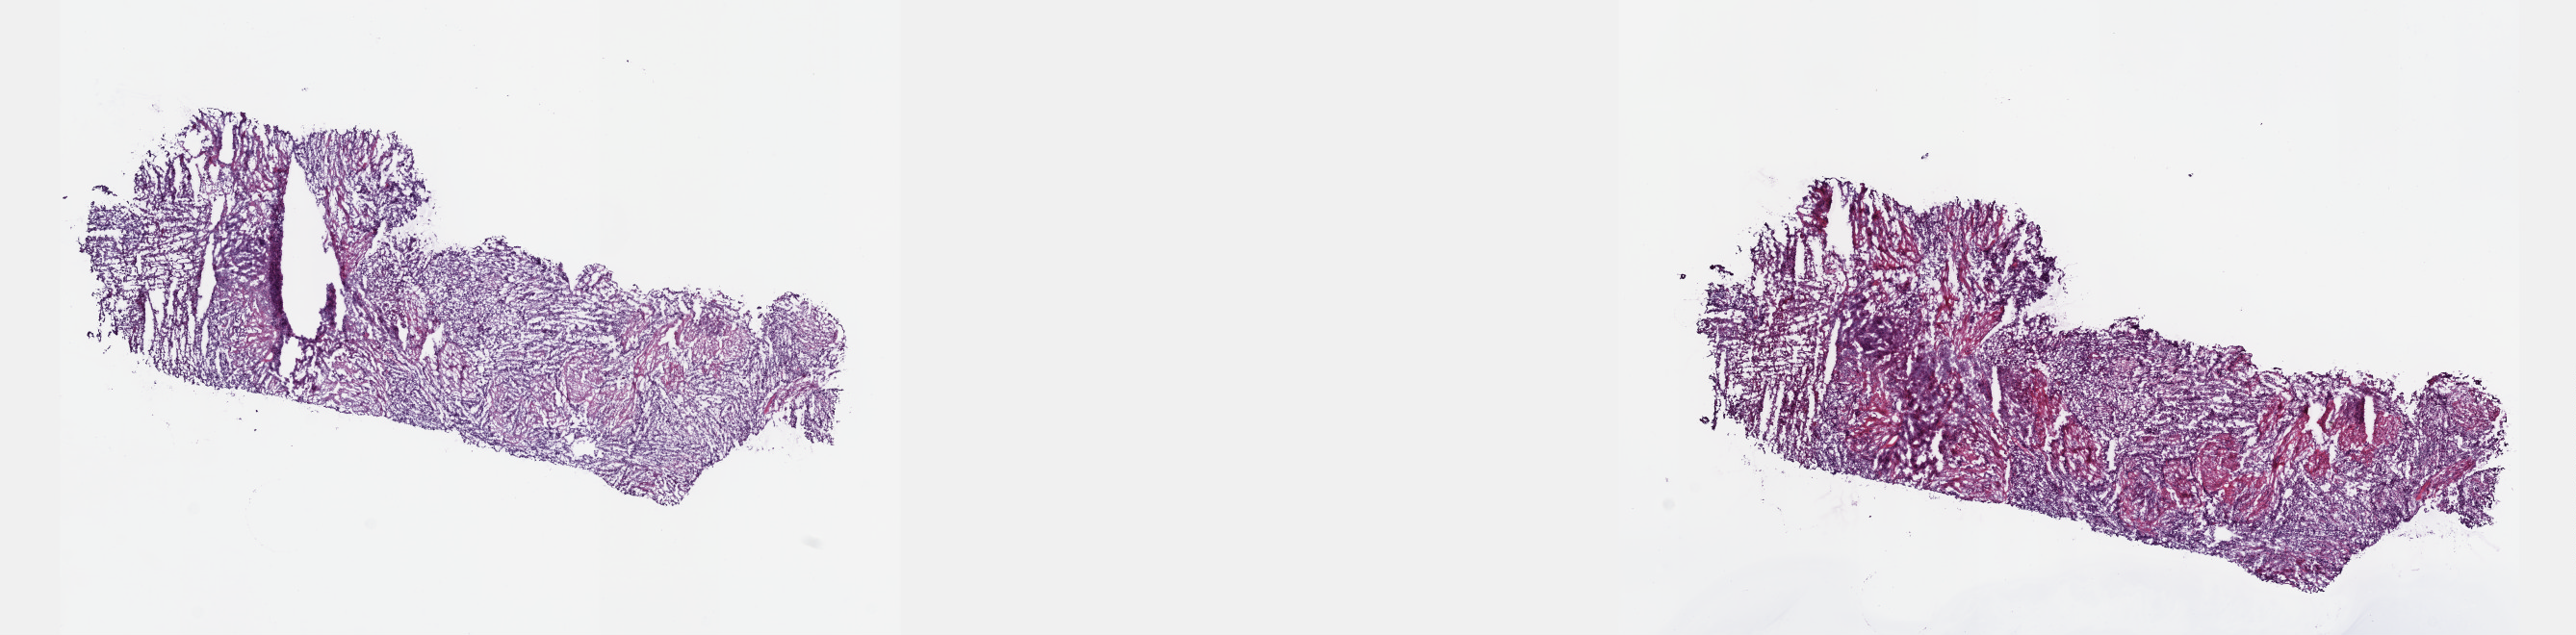
Digitized Hematoxylin and eosin (H&E) stained tissue section (whole slide) — low-resolution overview of the scanned area, about 21.6 x 5.3 mm; frozen section; primary tumour sample from the bladder. Patient: male, age at initial diagnosis 66 years.
Histologic diagnosis: Transitional cell carcinoma (dome of bladder).